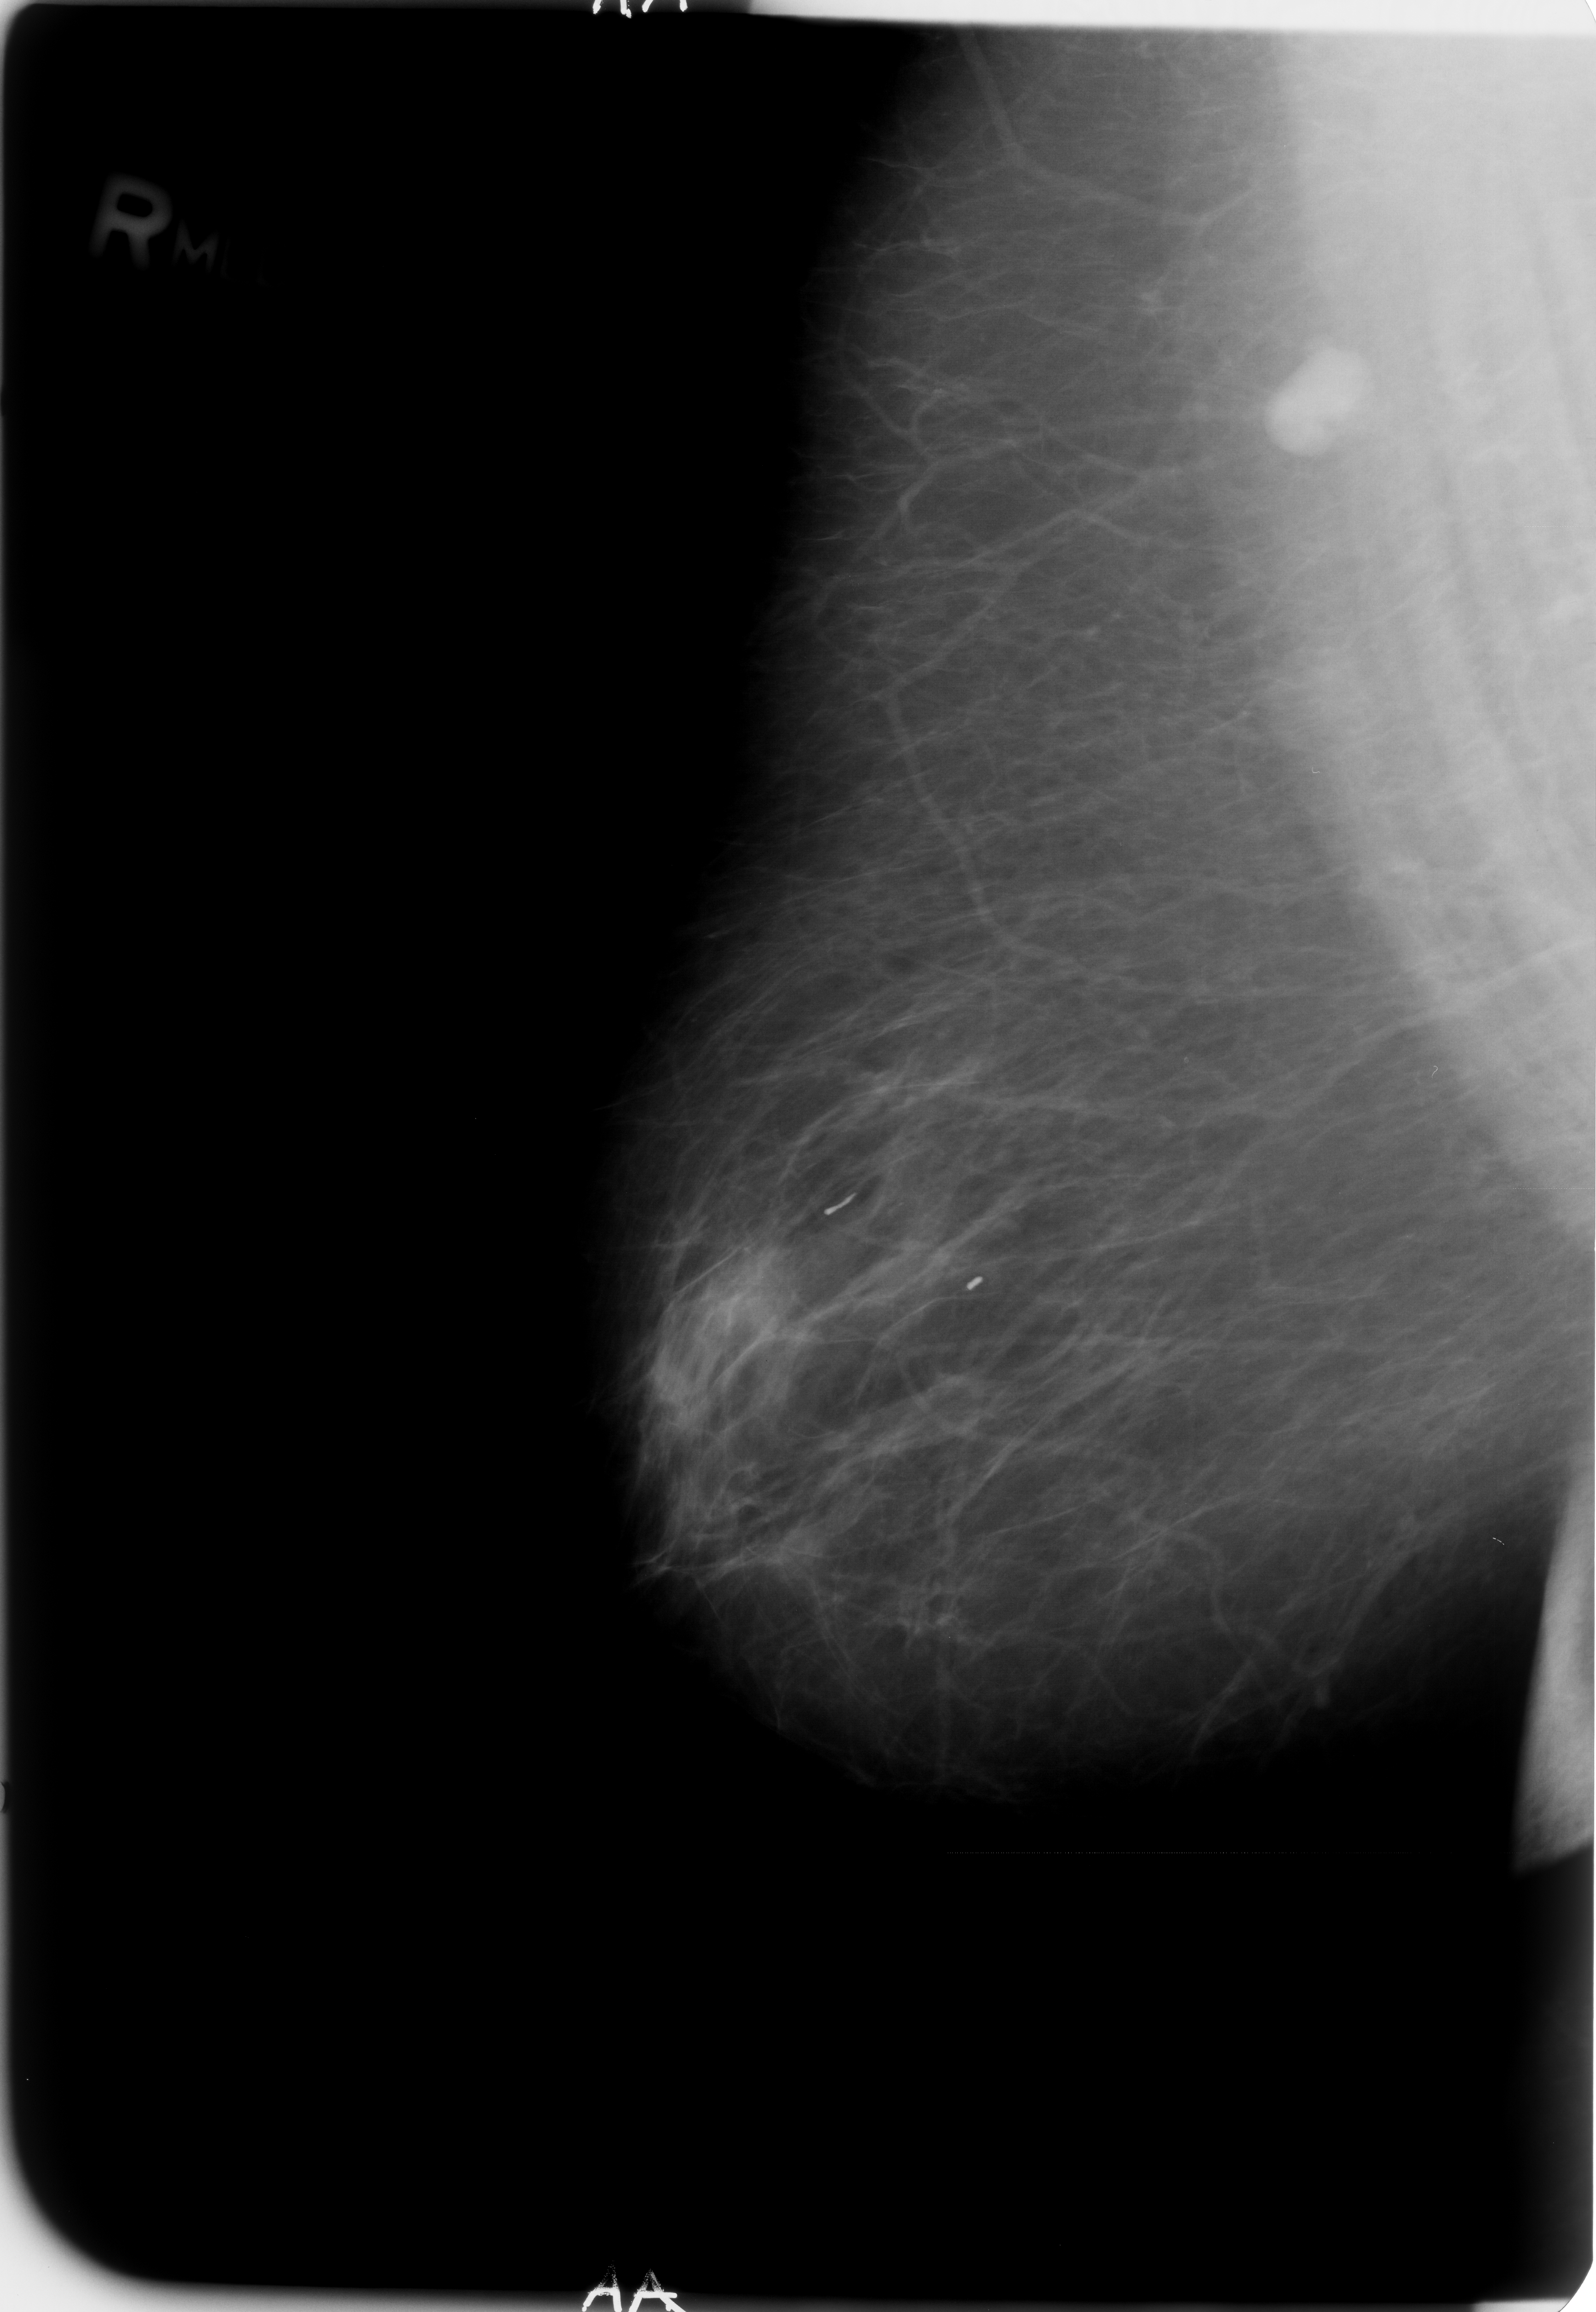
Scanned film-screen mammogram. Right breast. MLO view. BI-RADS breast density category 1 (scale 1–4). 1596 × 2312 image matrix.
Expert-marked regions of interest on this film, with their recorded descriptors:
- Finding 1 of 2: calcifications, morphology large rodlike, distribution segmental; BI-RADS assessment category 2; subtlety rating 5 on a 1 (subtle) to 5 (obvious) scale; benign; no additional work-up was recommended (outcome (as recorded, no biopsy): benign without callback): bounding box <798,1160,881,1237> (left, top, right, bottom; pixels)
- Finding 2 of 2: calcifications, morphology large rodlike, distribution segmental; BI-RADS assessment category 2; subtlety rating 5 on a 1 (subtle) to 5 (obvious) scale; benign; no additional work-up was recommended (outcome (as recorded, no biopsy): benign without callback): <946,1258,1004,1322>